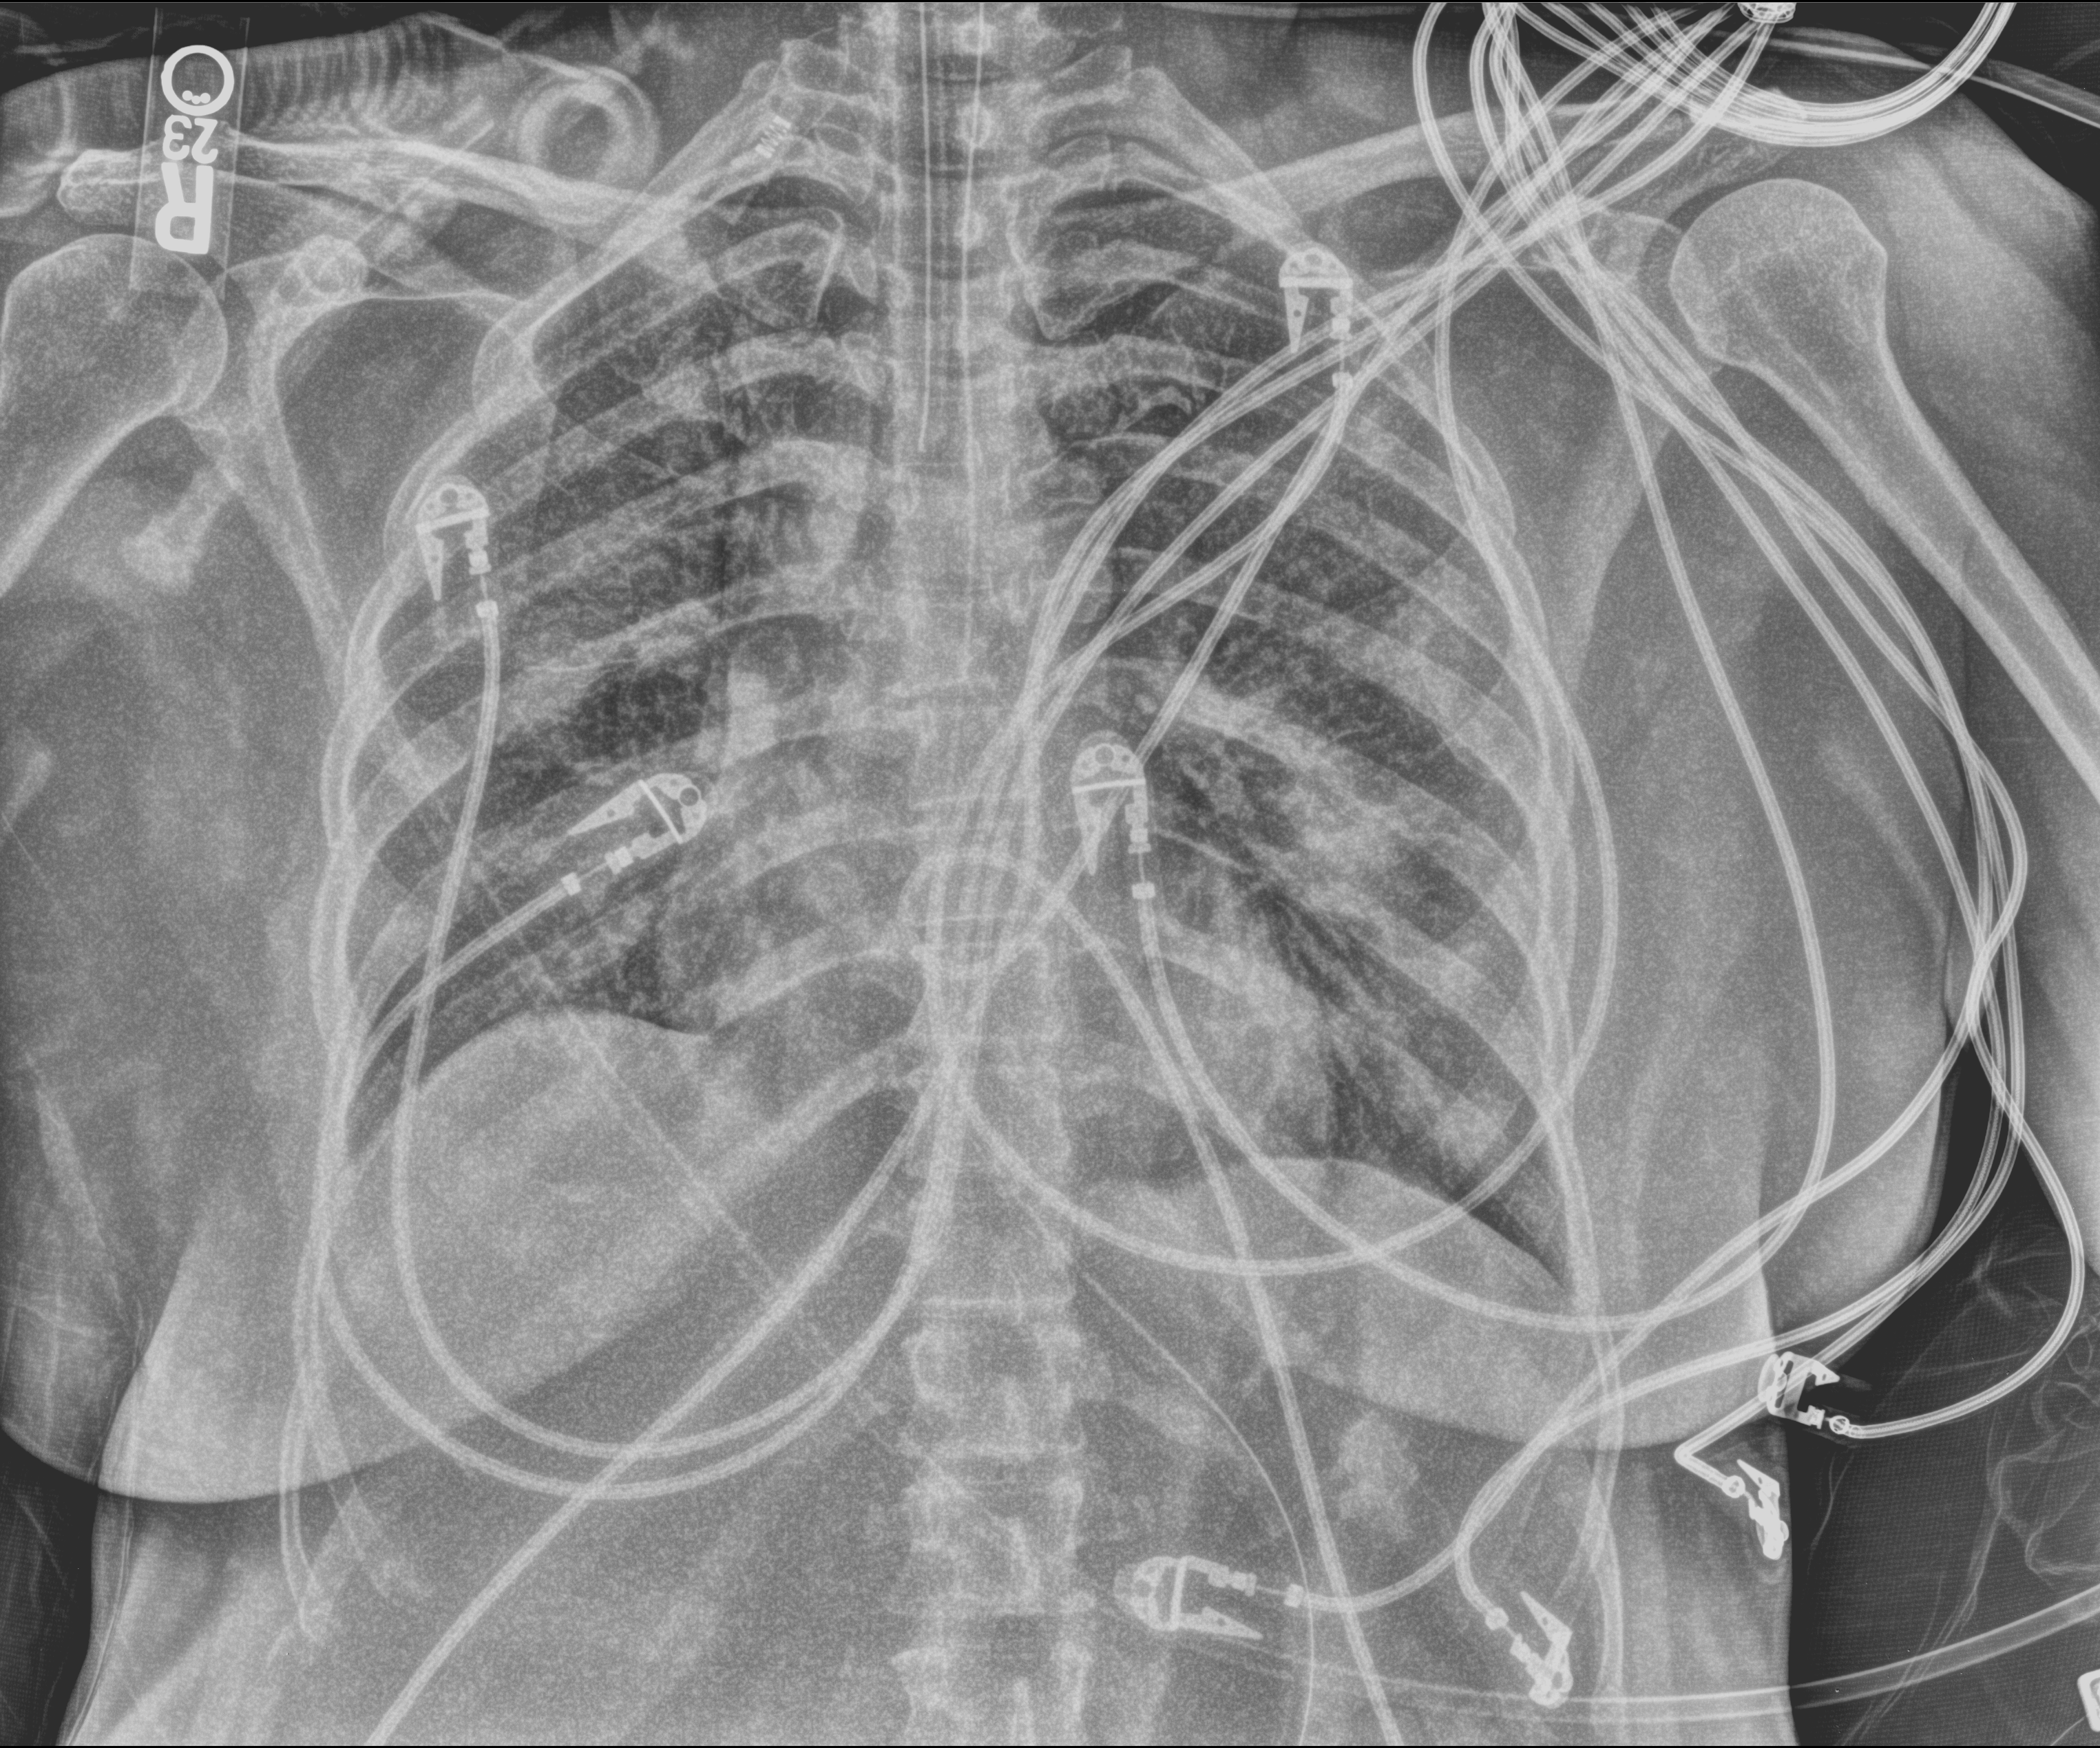
Bedside chest radiograph (computed radiography); anteroposterior (AP) projection. Male patient hospitalised with COVID-19, age 18–59 years.
Admission-level facts for this patient (not findings on this image; timing relative to this image not recorded): admitted to intensive care during this hospital stay: yes; smoking status (admission record): never.